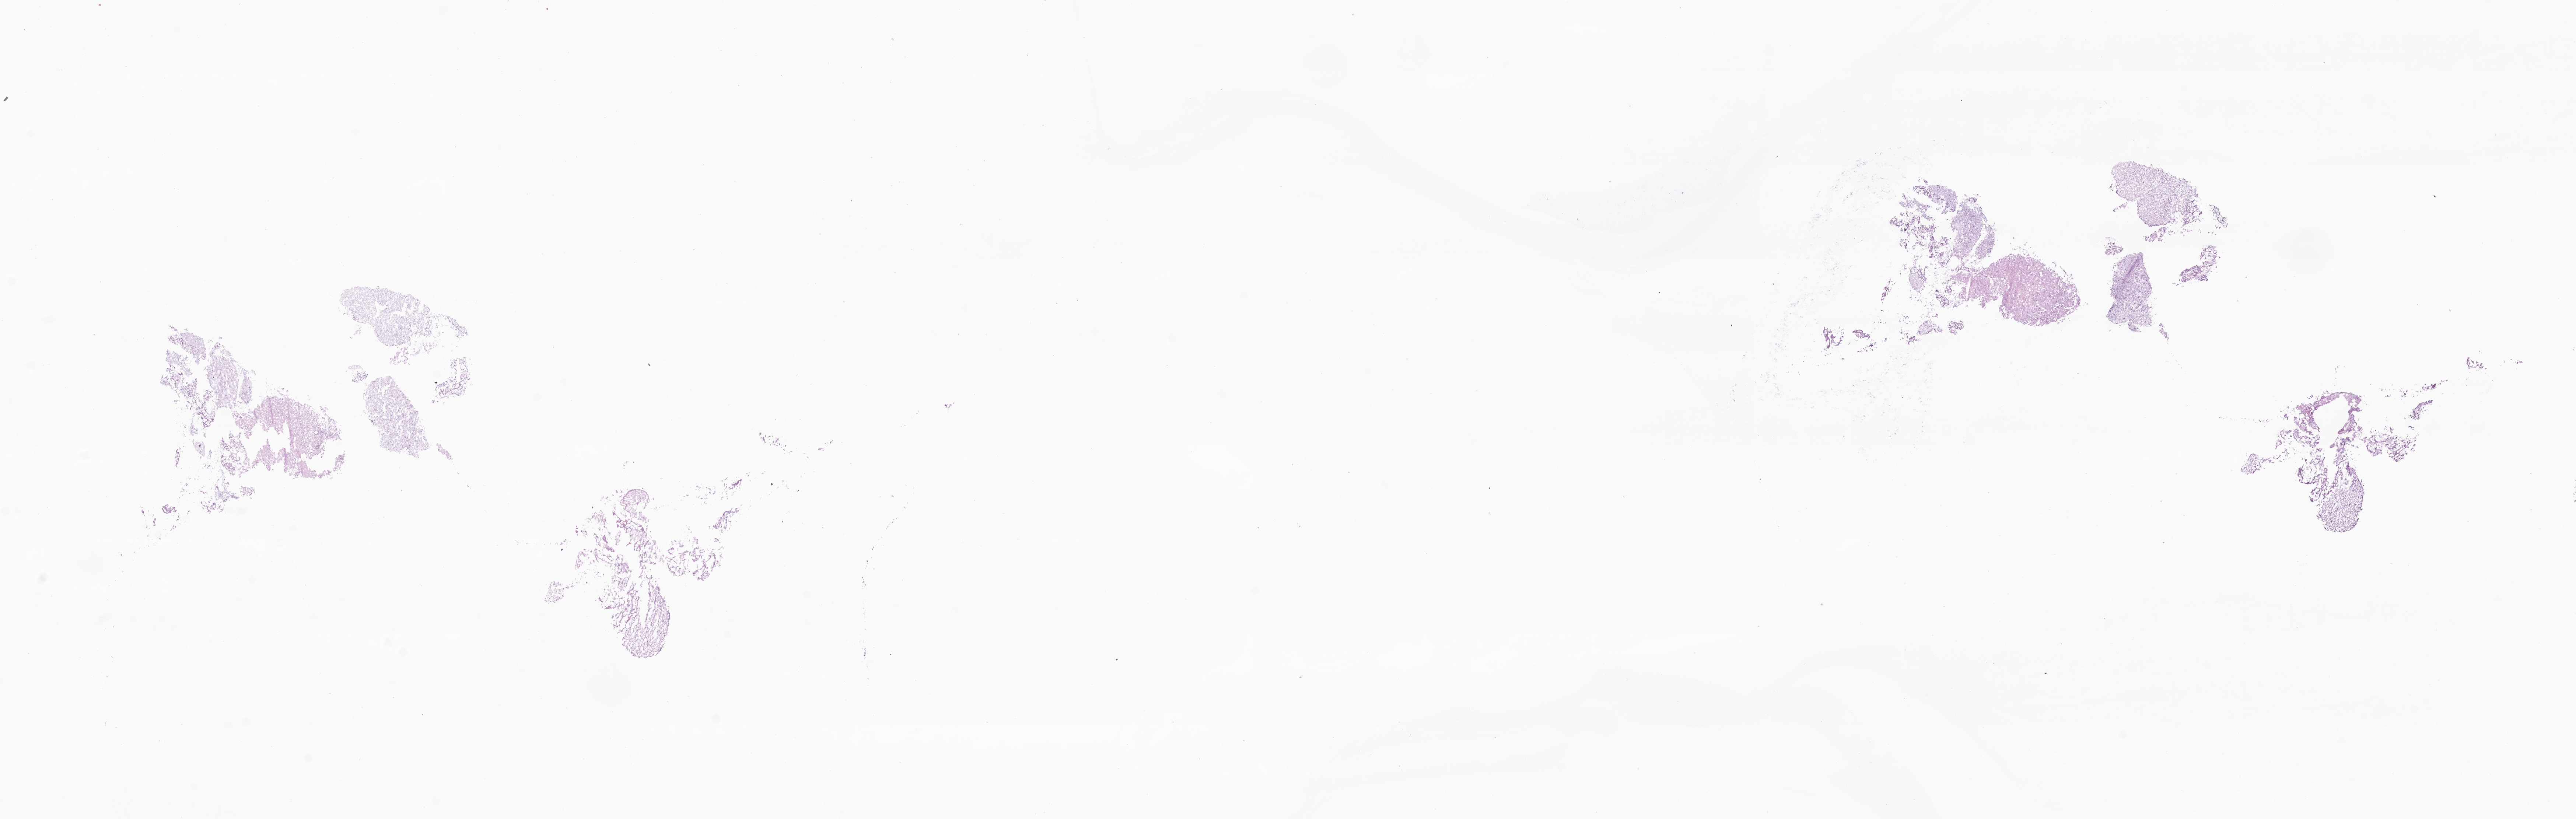
Whole-slide image, hematoxylin and eosin (H&E) stain of tumor tissue from the brain, whole scanned area (about 29.5 x 9.4 mm) shown as a low-resolution overview; cryosection (OCT / tissue freezing medium). Male patient, age 505 days (about 1.4 years).
- recorded diagnosis: Ganglioglioma, NOS